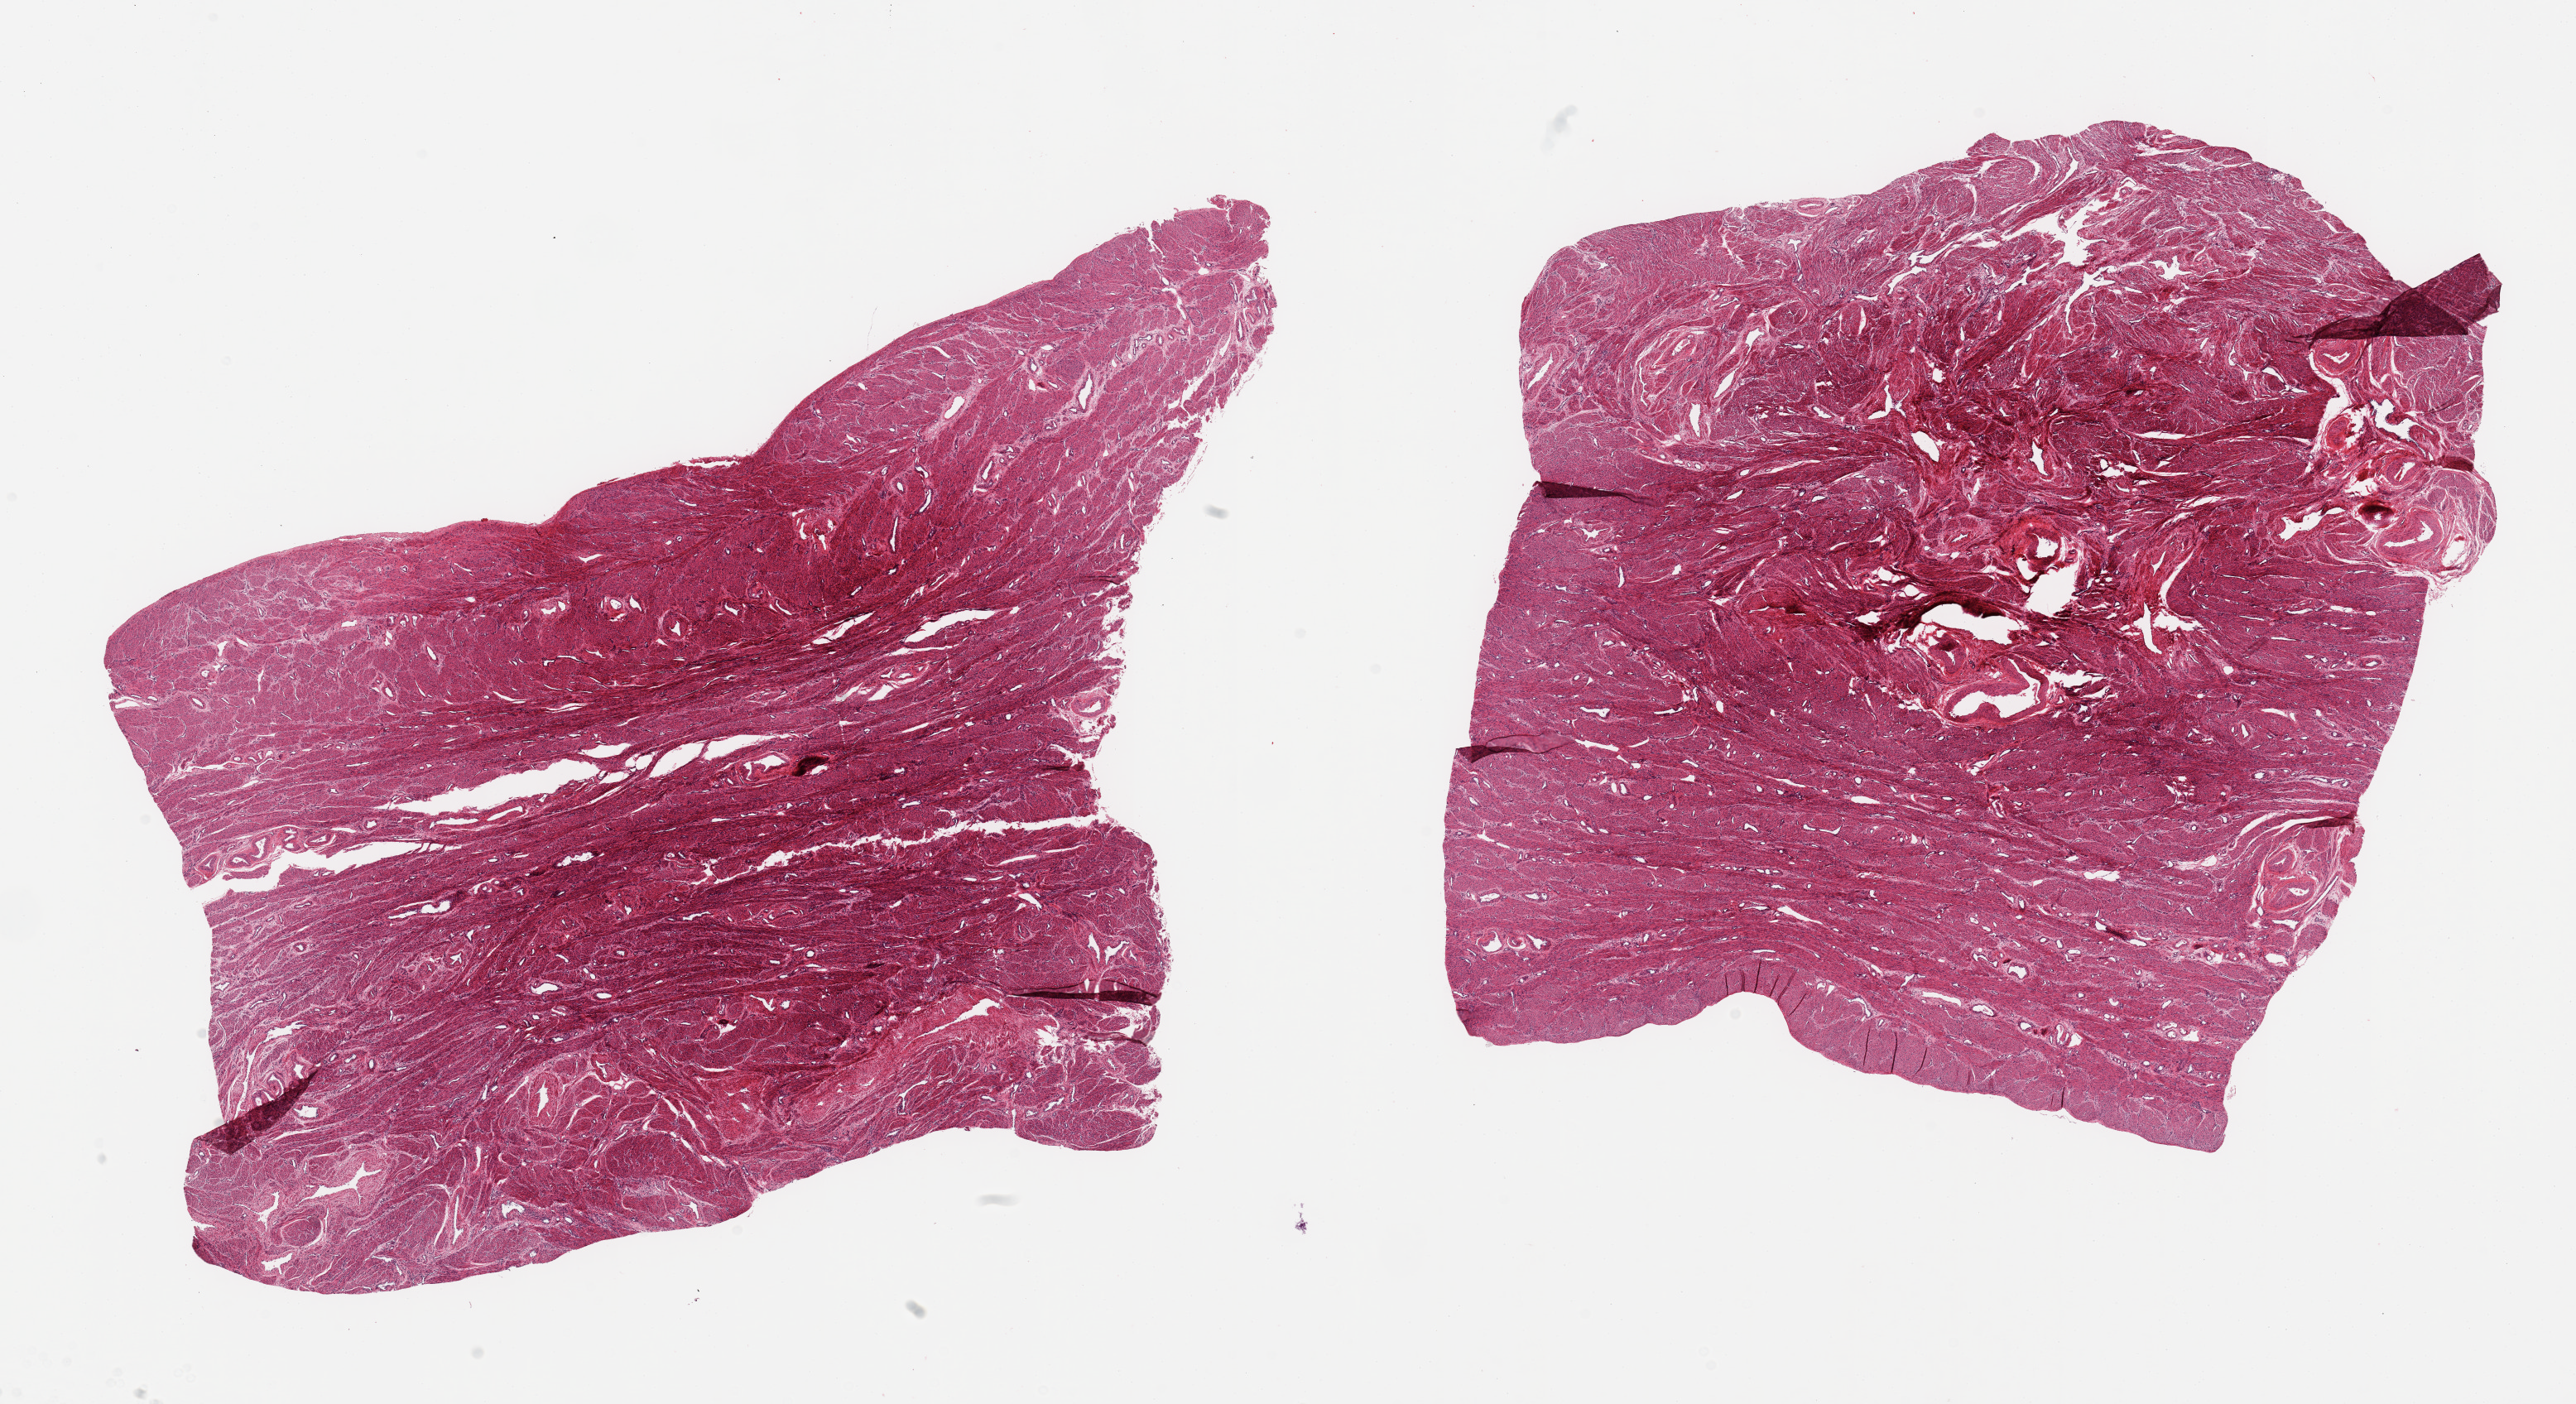
H&E whole-slide image — a low-resolution overview of the entire scanned area, about 24.6 x 13.4 mm; PAXgene-fixed paraffin-embedded (PFPE) section; target tissue: uterus; tissue donor sample. Female donor.
Reviewer comment on this tissue sample: 2 pieces; myometrium only in this section.